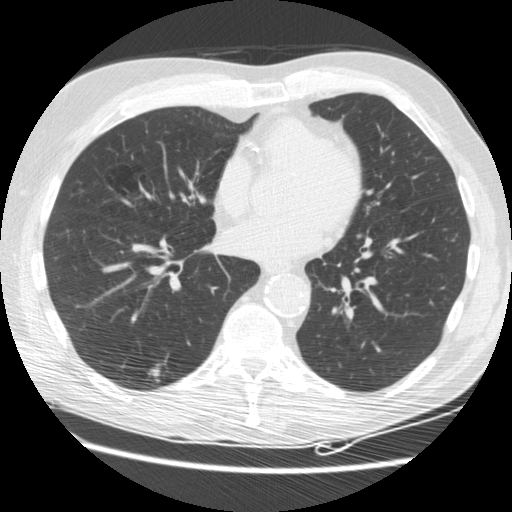
Low-dose screening chest CT, axial slice; third annual screen; lung window (W 1500 / L -600 HU); 2.5 mm slice thickness; standard (soft-tissue) reconstruction kernel (STANDARD); slice 101 of 176 in the series. Male participant, aged 62 years at enrolment. Current smoker at enrolment.
Lesion marked by an expert reader, bounding box (x1, y1, x2, y2) in pixels: (138, 352, 184, 395). The screening reader recorded 3 non-calcified nodules or masses ≥4 mm on this exam (right lower lobe, right lower lobe, right lower lobe); which of them this box marks is not recorded. Participant outcome: lung cancer diagnosed 33 days after this screen — adenocarcinoma, NOS, right lower lobe, moderately differentiated (G2), stage IIIB (AJCC 6th edition), 15 mm at pathology.